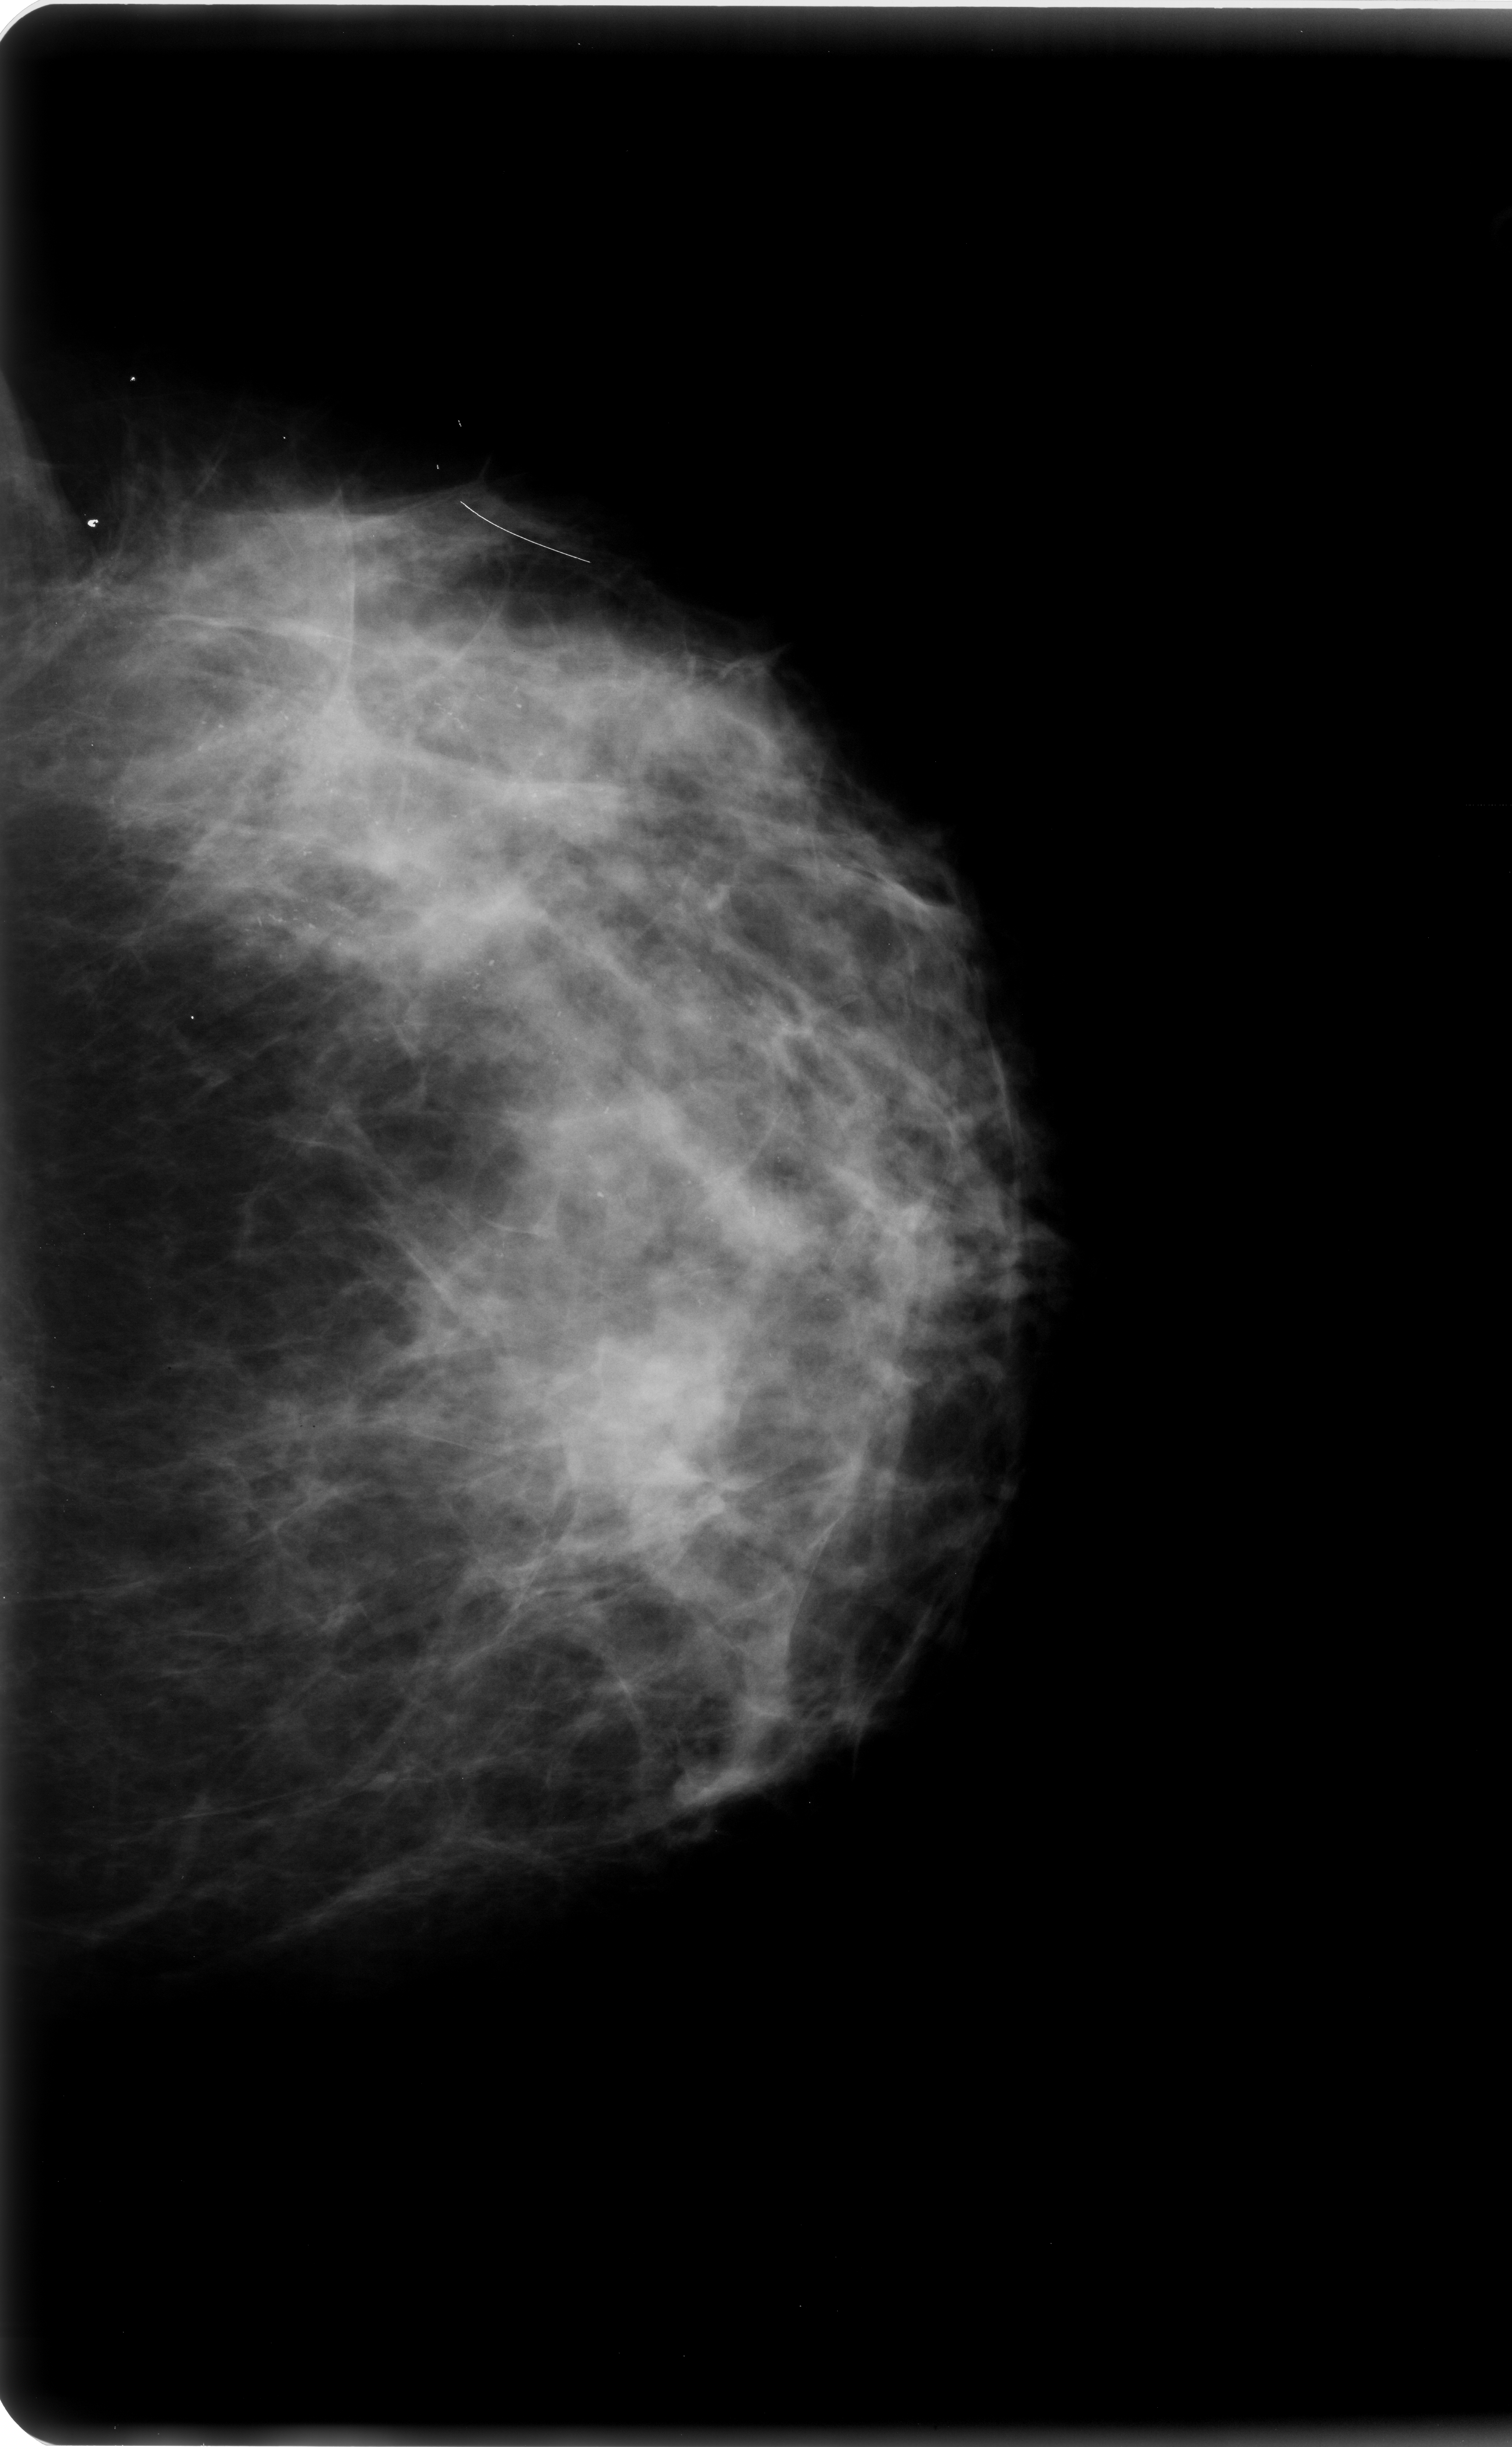
Digitized screen-film mammogram; left breast; craniocaudal (CC) view; BI-RADS breast density category 2 (scale 1–4); 1512 × 2447 image matrix.
Marked abnormalities (boxes around the expert regions of interest):
- calcifications, morphology pleomorphic, distribution regional; BI-RADS assessment category 5; pathology result (as recorded, not read from the image): malignant: box from (x=25, y=460) to (x=955, y=1650) px